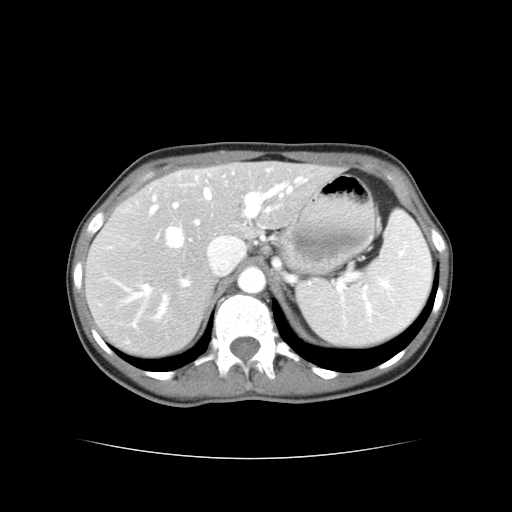
Contrast-enhanced abdominal CT, one axial slice. Position 27 of 38 along the scan axis. Reconstruction kernel STANDARD. 120 kVp. Intravenous contrast given. Soft-tissue window (W 400 / L 40 HU). 512 × 512 image matrix, field of view 340 × 340 mm. Female patient, age 54 years. Case-level facts recorded for this patient, not image findings: diagnosis: colorectal cancer liver metastases, imaged before liver resection; multiple liver metastases: yes; largest metastasis: 1.1 cm.
Outlined on this slice (outlined manually by an expert reader):
- hepatic veins: bounding box <158,188,292,318> (left, top, right, bottom; pixels)
- liver: <87,163,335,357>
- planned liver remnant (the part of the liver to remain after resection): <211,163,335,236>
- portal vein (with intrahepatic branches): <130,179,303,301>